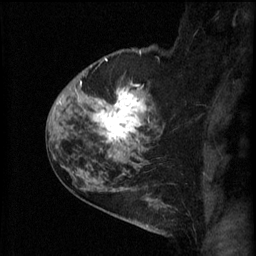
Breast MRI (dynamic contrast-enhanced), one sagittal slice. Slice 44 of 60 in the series (ordered by position). 3 images stored at this slice position (order not interpretable as contrast timing). 1.5 T. TE 4.2 ms, TR 11 ms. 2.3 mm slice thickness. 256 × 256 image matrix, field of view 180 × 180 mm. Female patient, age 52 years.
Outlined on this slice (semi-automatic segmentation, software-assisted and operator-edited):
- analysis volume of interest (the breast-tissue region the enhancement analysis was run in; not a lesion): bounding box (x1, y1, x2, y2) in pixels: (86, 76, 164, 157)
- tumour enhancement mask (voxels above the 70 % enhancement threshold inside the analysis volume of interest): (91, 84, 149, 155)